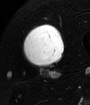
MRI of an extremity soft-tissue mass, one axial slice; position 41 of 65 along the scan axis; T2-weighted fat-saturated; MR volume resampled by the dataset authors to the PET/CT grid (not the native acquisition matrix); 90 × 105 image matrix, field of view 88 × 103 mm. Male patient. Case-level facts recorded for this patient, not image findings: histological type: mixoid liposarcoma; grade: low; site of the primary tumour: left thigh.
Annotated regions visible in this slice (expert contour drawn on MRI and transferred to this co-registered scan by the dataset authors):
- gross tumour volume (mass): box from (x=21, y=25) to (x=65, y=70) px